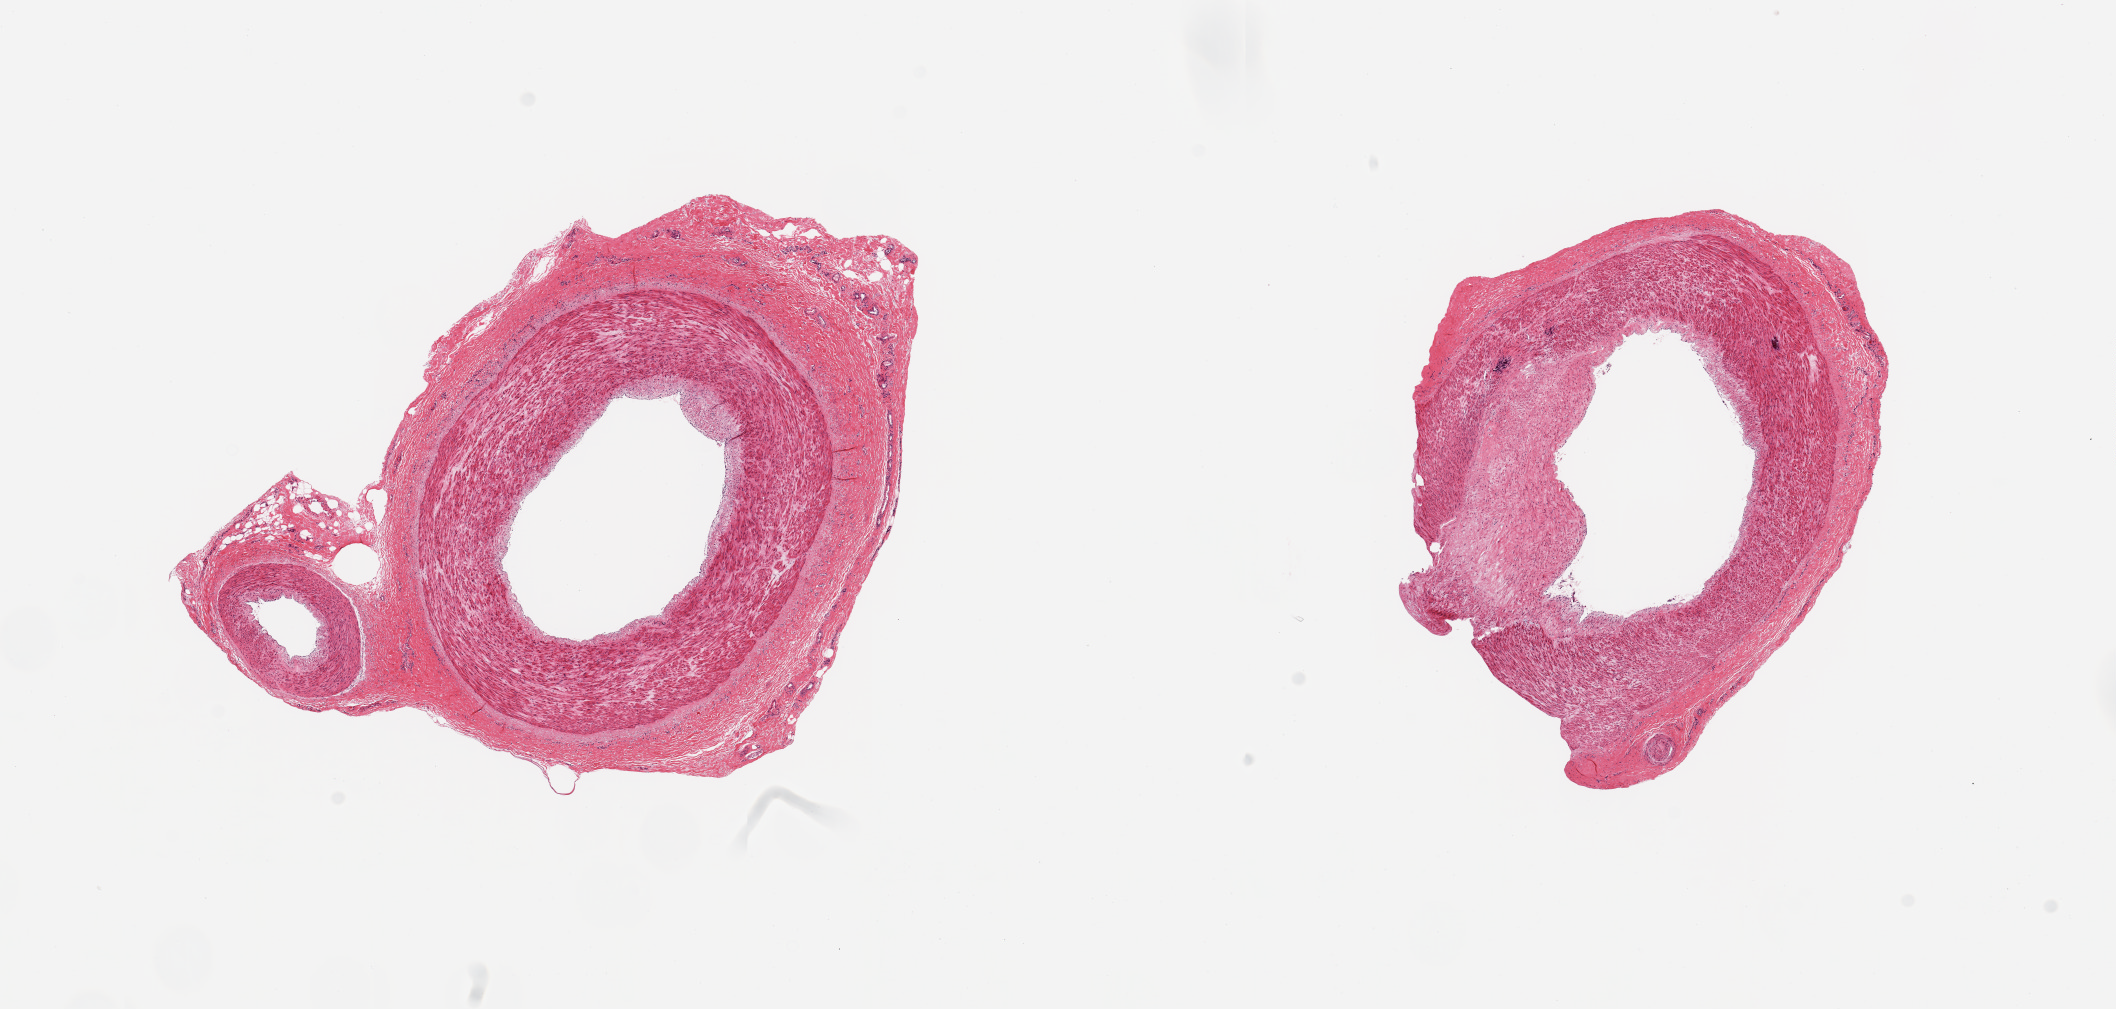
Whole-slide image, haematoxylin and eosin stain, brightfield, shown as a low-resolution overview of the whole scanned area (about 16.7 x 8.0 mm, from a 20x scan); PAXgene-fixed, paraffin-embedded tissue; section of tibial artery (target tissue); donor tissue sample. Donor sex: male.
* review note (as recorded): 2 pieces; well dissected